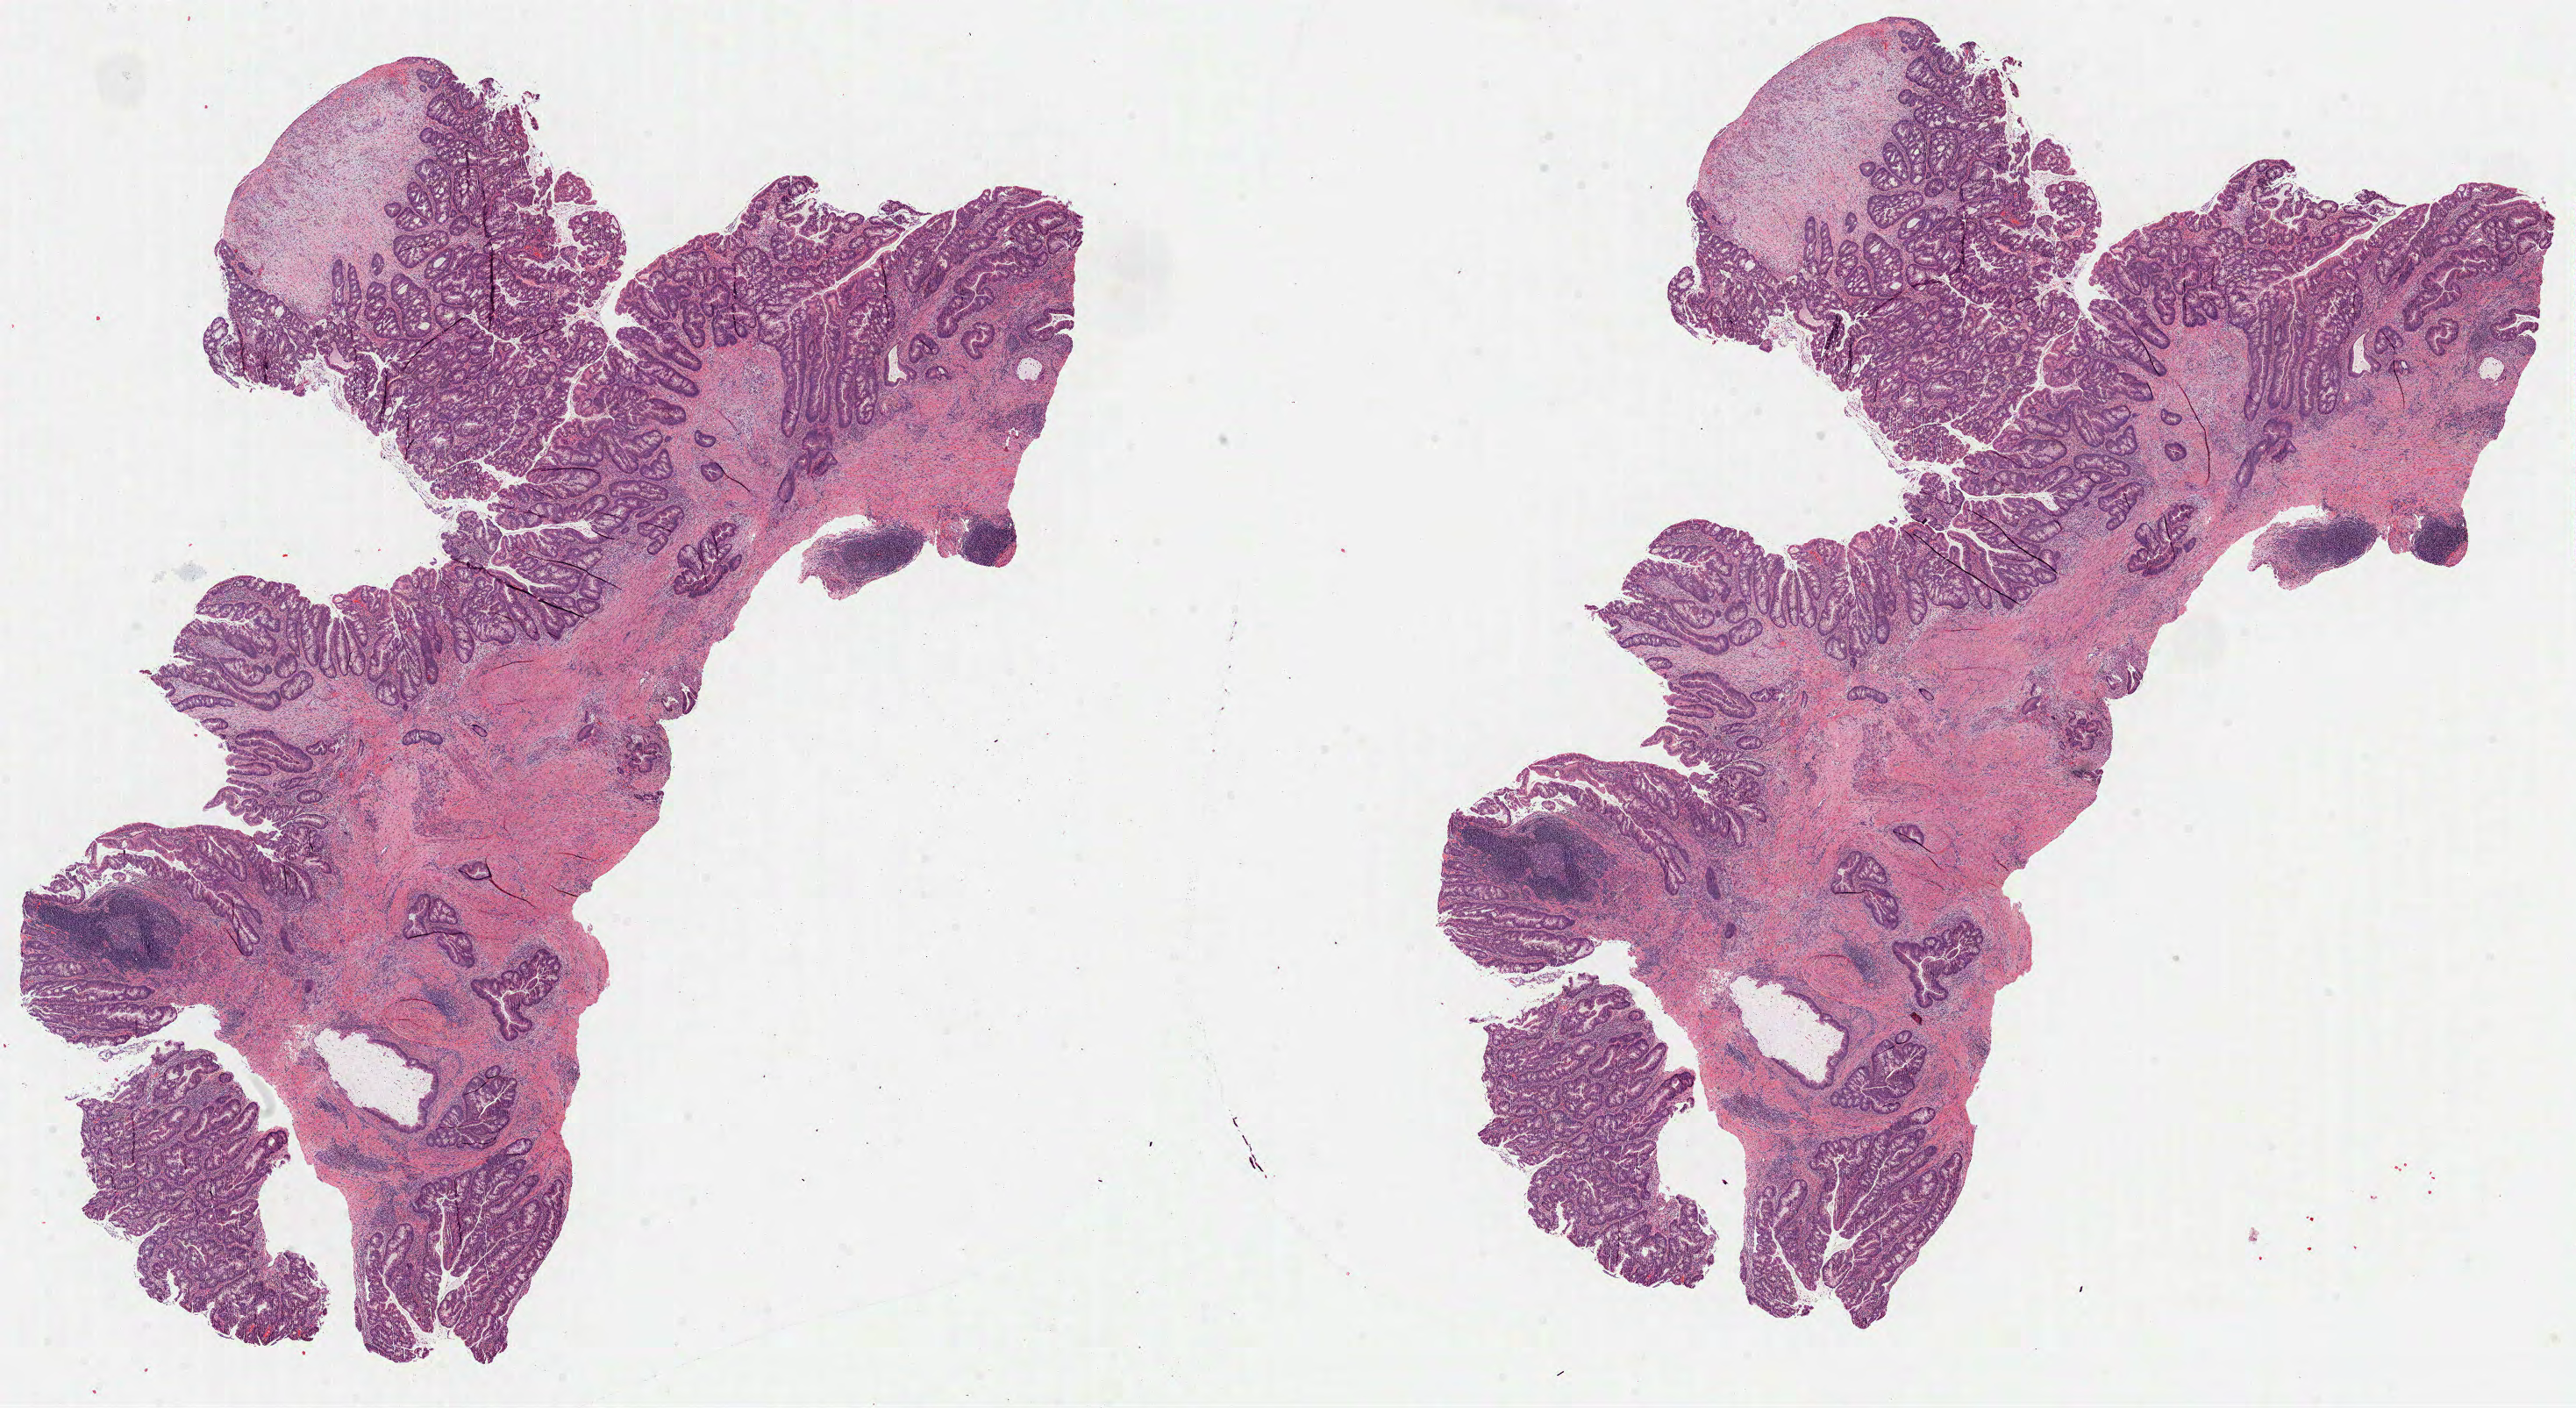
Whole-slide histology image, H&E — whole scanned area (about 23.7 x 12.9 mm) shown as a low-resolution overview; FFPE section; sample: primary tumour, colon. Patient: female, age at initial diagnosis 66 years.
Pathologic diagnosis: Adenocarcinoma, NOS. AJCC pathologic stage: IIIB.